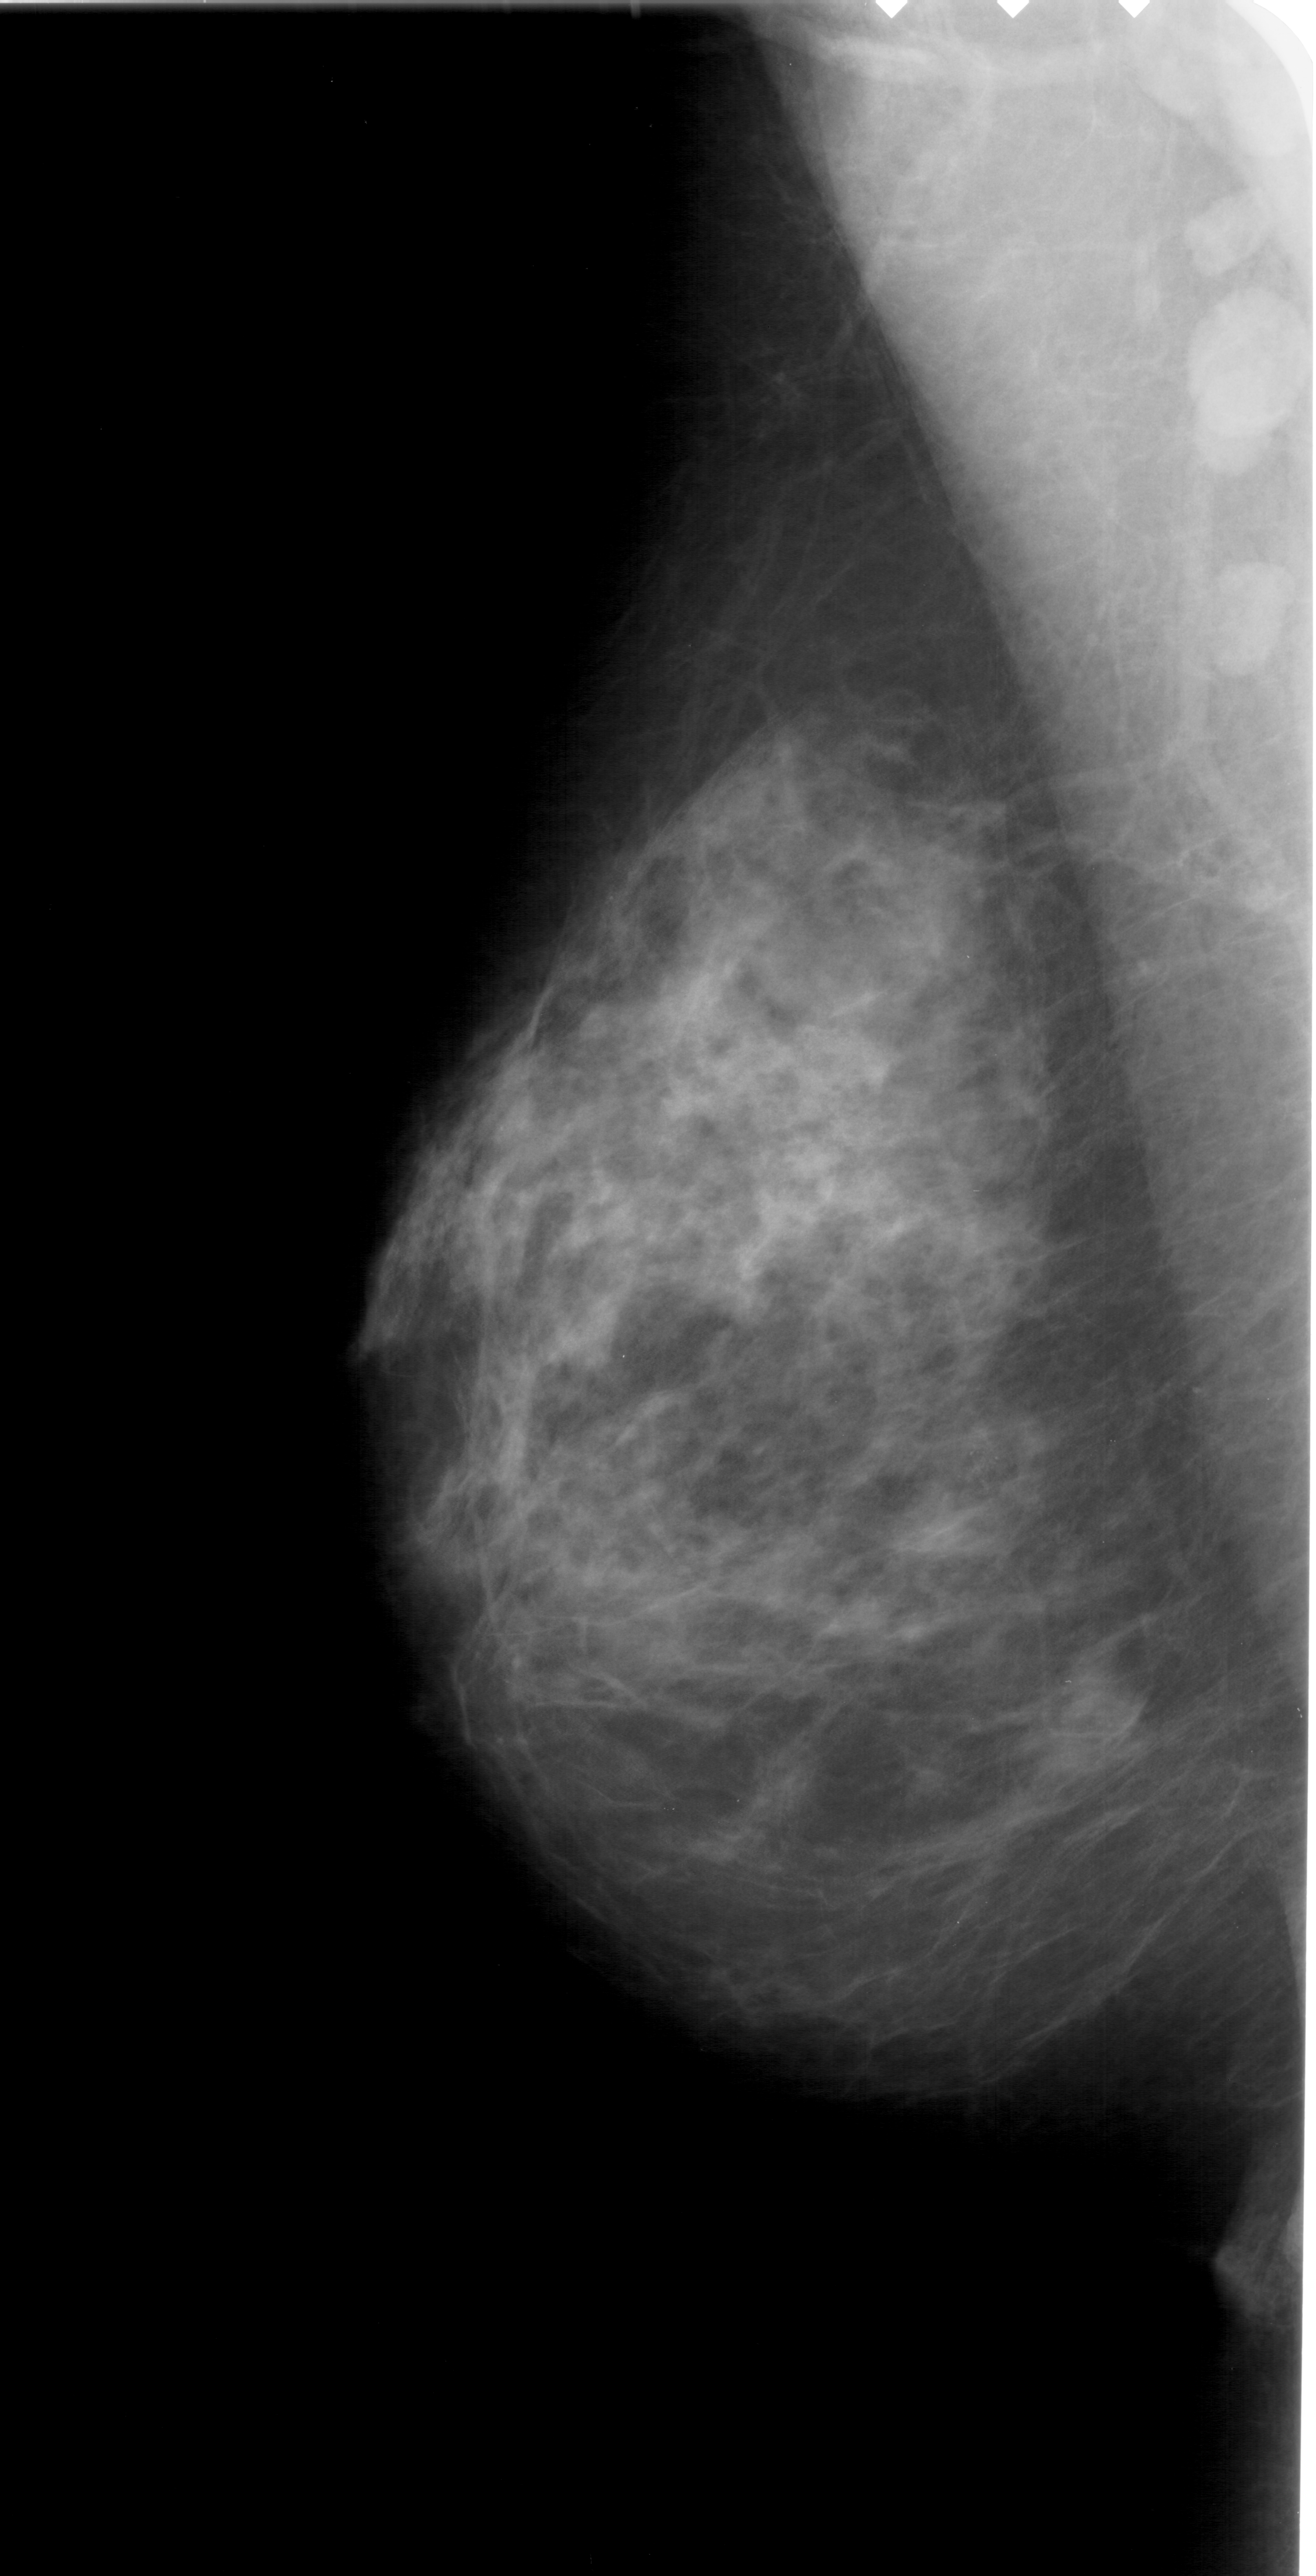
Scanned film-screen mammogram; left breast; MLO view; 1316 × 2576 image matrix.
Marked abnormalities (boxes around the expert regions of interest):
- calcifications, morphology pleomorphic, distribution clustered; BI-RADS assessment category 4; subtlety rating 2 on a 1 (subtle) to 5 (obvious) scale; pathology result (as recorded, not read from the image): benign: bounding box <947,1430,1011,1497> (left, top, right, bottom; pixels)